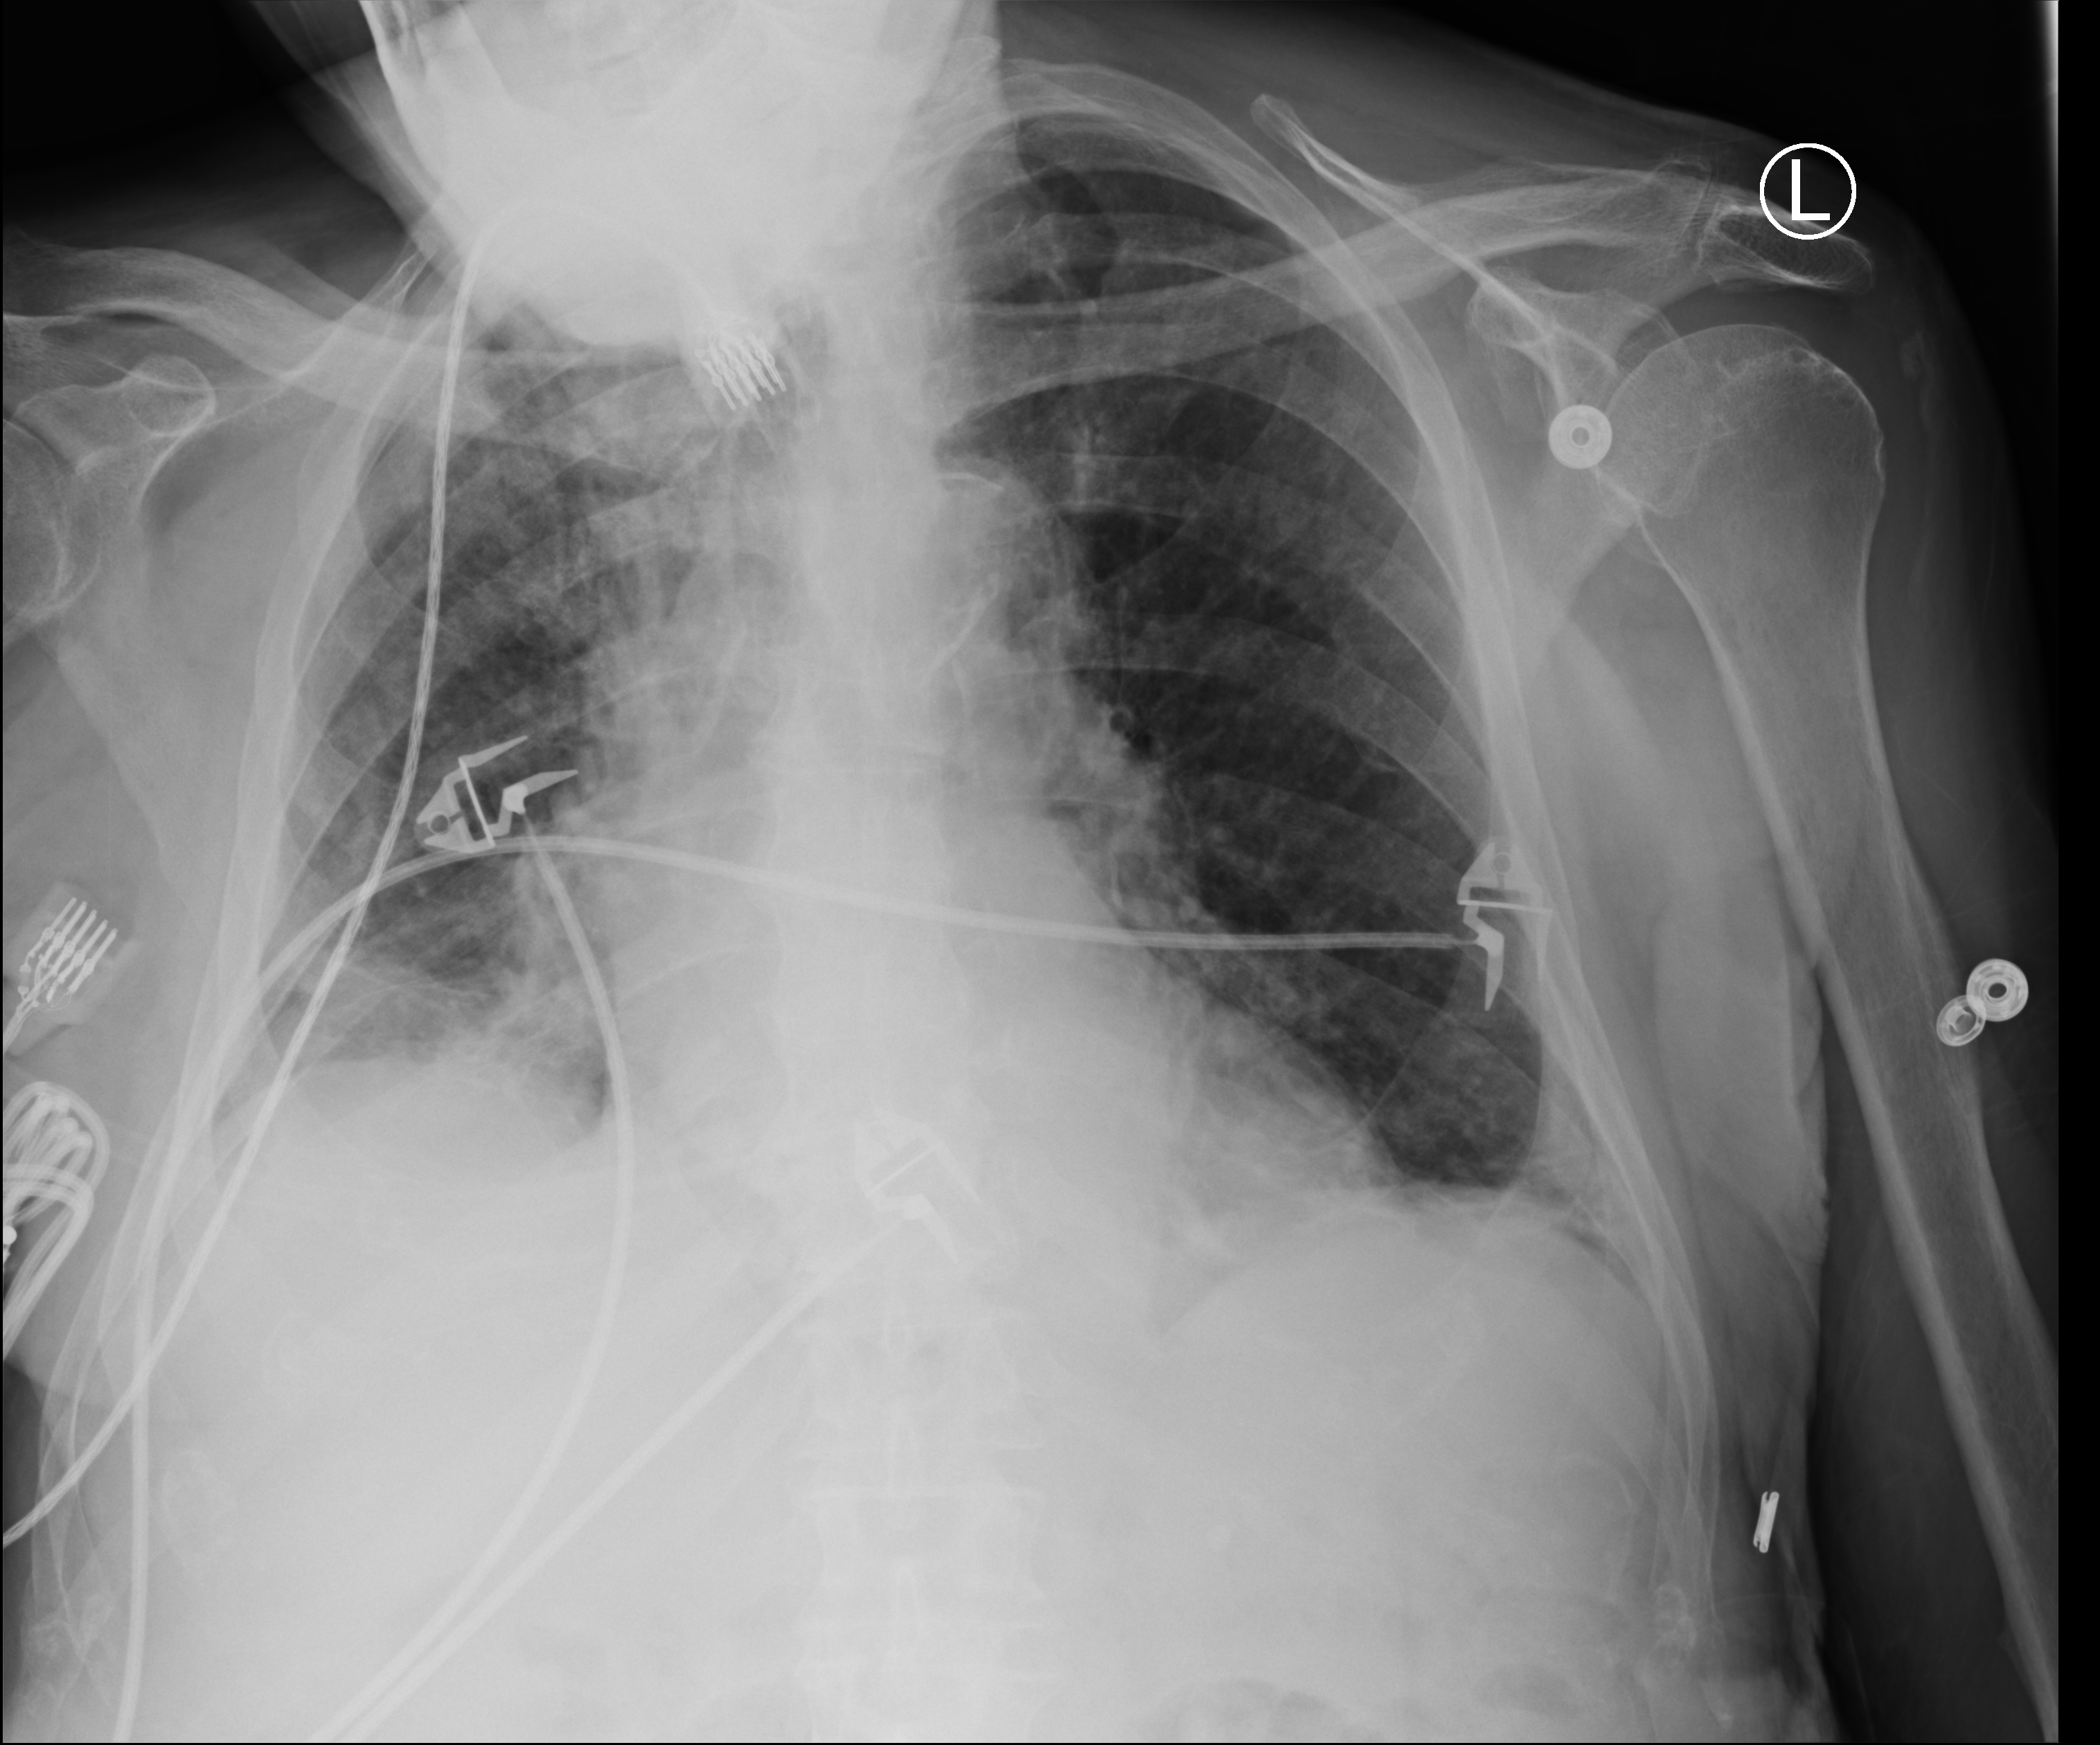
Chest X-ray (portable); anteroposterior (AP) projection. Male patient hospitalised with COVID-19, age 75–90 years.
Admission-level facts for this patient (not findings on this image; timing relative to this image not recorded):
- length of hospital stay: 28 days
- smoking status (admission record): never